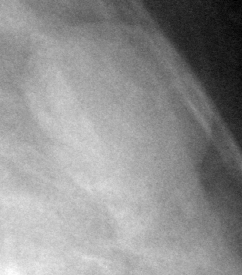
Cropped region of a digitized screen-film mammogram centred on a radiologist-marked abnormality, left breast, MLO view, BI-RADS breast density category 3 (scale 1–4).
Marked abnormality: mass, shape oval, margins circumscribed; BI-RADS assessment category 3; subtlety rating 5 on a 1 (subtle) to 5 (obvious) scale; pathology result (as recorded, not read from the image): benign.